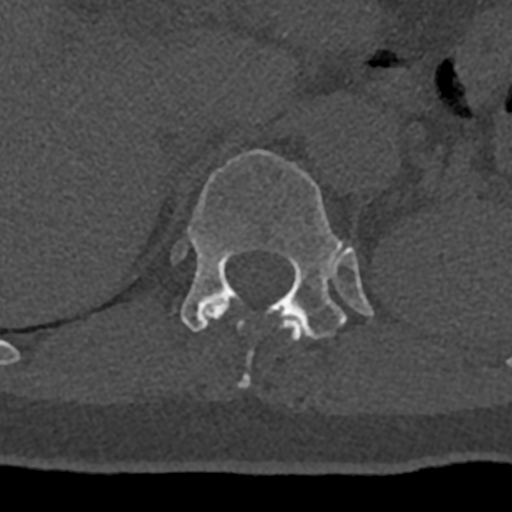
CT including the spine, one axial slice. Slice 508 of 797 in the series (ordered by position). 120 kVp. Bone window (W 1800 / L 400 HU). 0.5 mm slice thickness. 512 × 512 image matrix. Male patient, age 74 years. Case-level facts recorded for this patient, not image findings: primary cancer: renal; vertebrae with lytic lesions (as recorded): T10, L1, L2, L3, L4, L5.
Annotated regions visible in this slice (semi-automatic segmentation, software-assisted and operator-edited):
- T11 vertebra: bounding box <205,302,304,388> (left, top, right, bottom; pixels)
- T12 vertebra: <172,149,374,339>